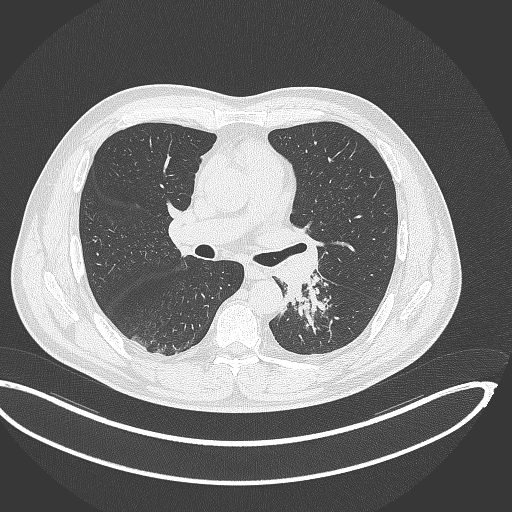
Chest CT, one axial slice. Slice 204 of 362 in the series (ordered by position). 120 kVp. Lung window (W 1500 / L -600 HU). 512 × 512 image matrix, field of view 442 × 442 mm. Patient: male, 50 years. Case-level facts recorded for this patient, not image findings: clinical TNM (as recorded): T2a N3 M0.
Annotated regions visible in this slice (rectangle marked by the reading radiologist):
- lung tumour (recorded histology: squamous cell carcinoma): bounding box (x1, y1, x2, y2) in pixels: (280, 273, 328, 324)